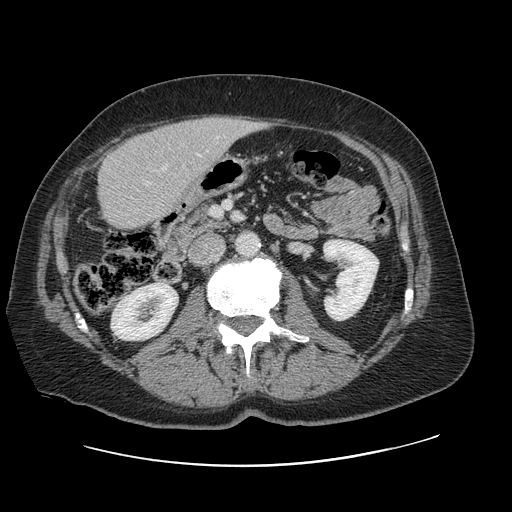
Contrast-enhanced abdominal CT, one axial slice. Position 30 of 138 along the scan axis. Intravenous contrast given. Soft-tissue window (W 400 / L 40 HU). 512 × 512 image matrix. Male patient, age 71 years. Case-level facts recorded for this patient, not image findings: diagnosis: colorectal cancer liver metastases, imaged before liver resection; multiple liver metastases: no; largest metastasis: 3.3 cm.
Structures marked on this image (outlined manually by an expert reader):
- hepatic veins: bounding box <199,136,218,156> (left, top, right, bottom; pixels)
- liver: <99,118,258,229>
- planned liver remnant (the part of the liver to remain after resection): <99,133,183,229>
- portal vein (with intrahepatic branches): <163,167,166,170>